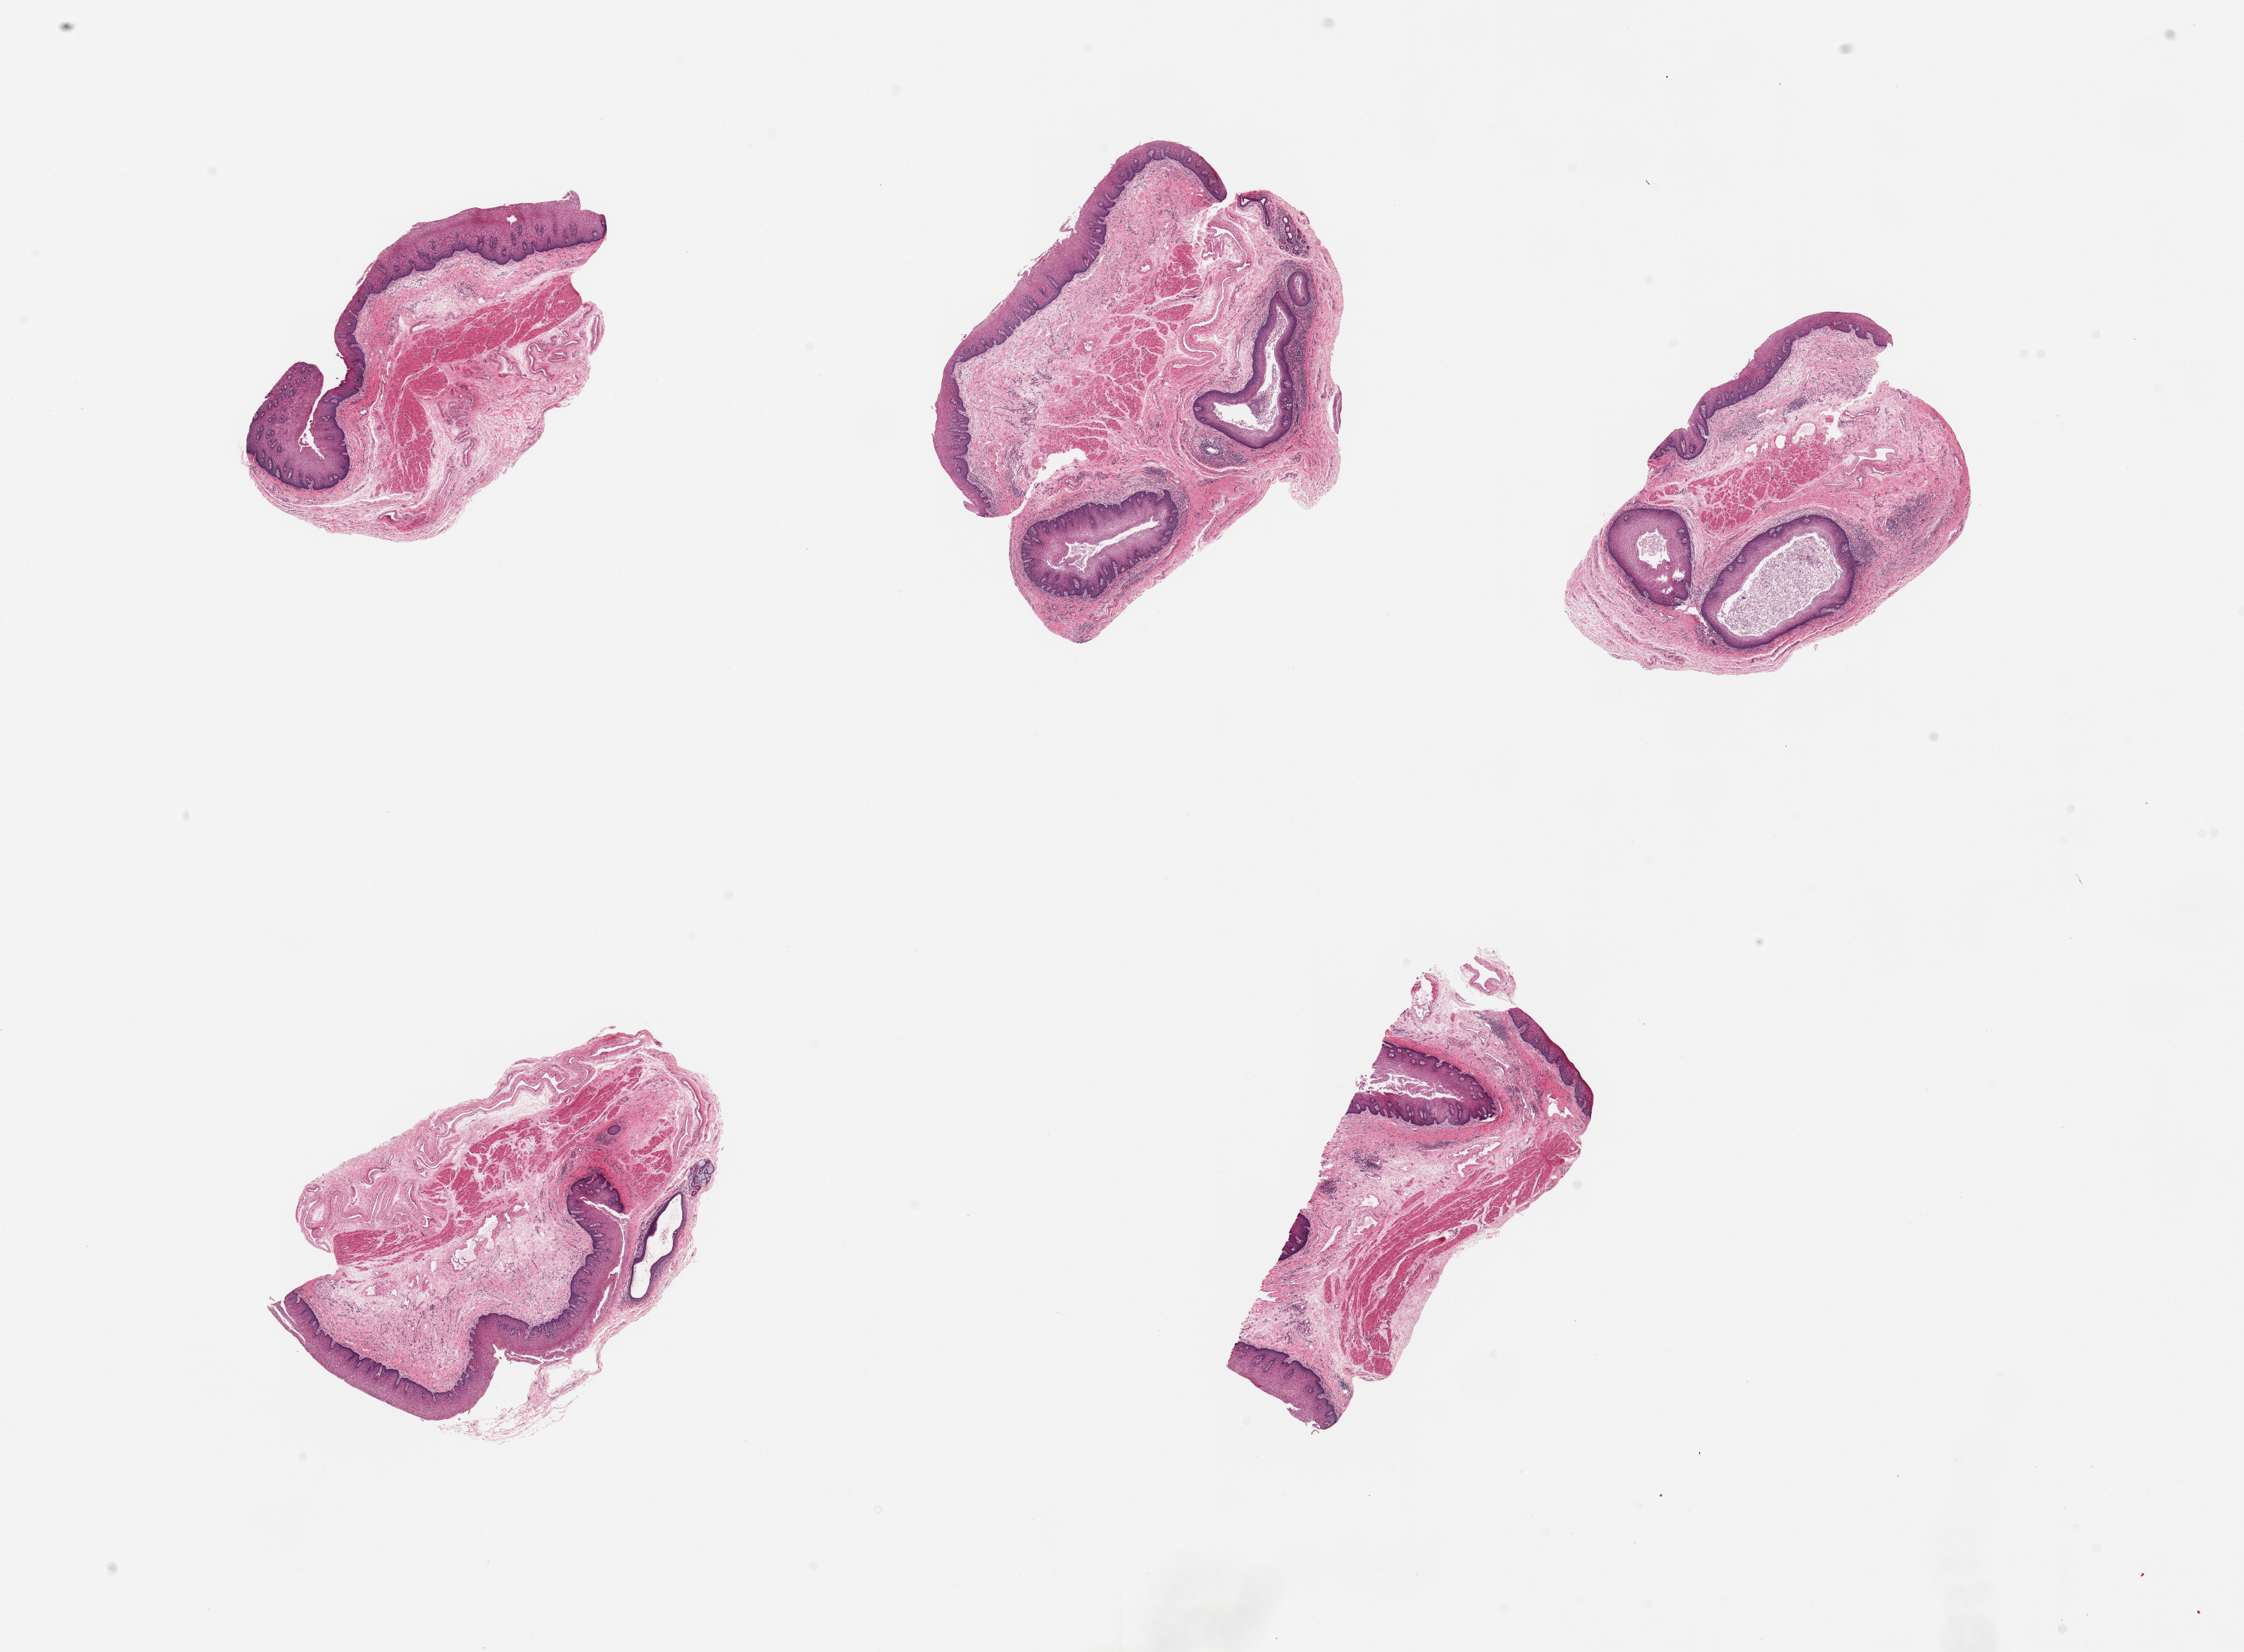
Whole-slide image, H&E stain, low-resolution overview of the scanned area, about 23.6 x 17.4 mm (acquisition: 20x scan), PAXgene-fixed paraffin-embedded (PFPE) section, target tissue: esophageal mucous membrane, tissue donor sample. Female donor.
- pathologist's review note for this sample: 5 pieces; pseudodiverticulosis with active chronic inflammation